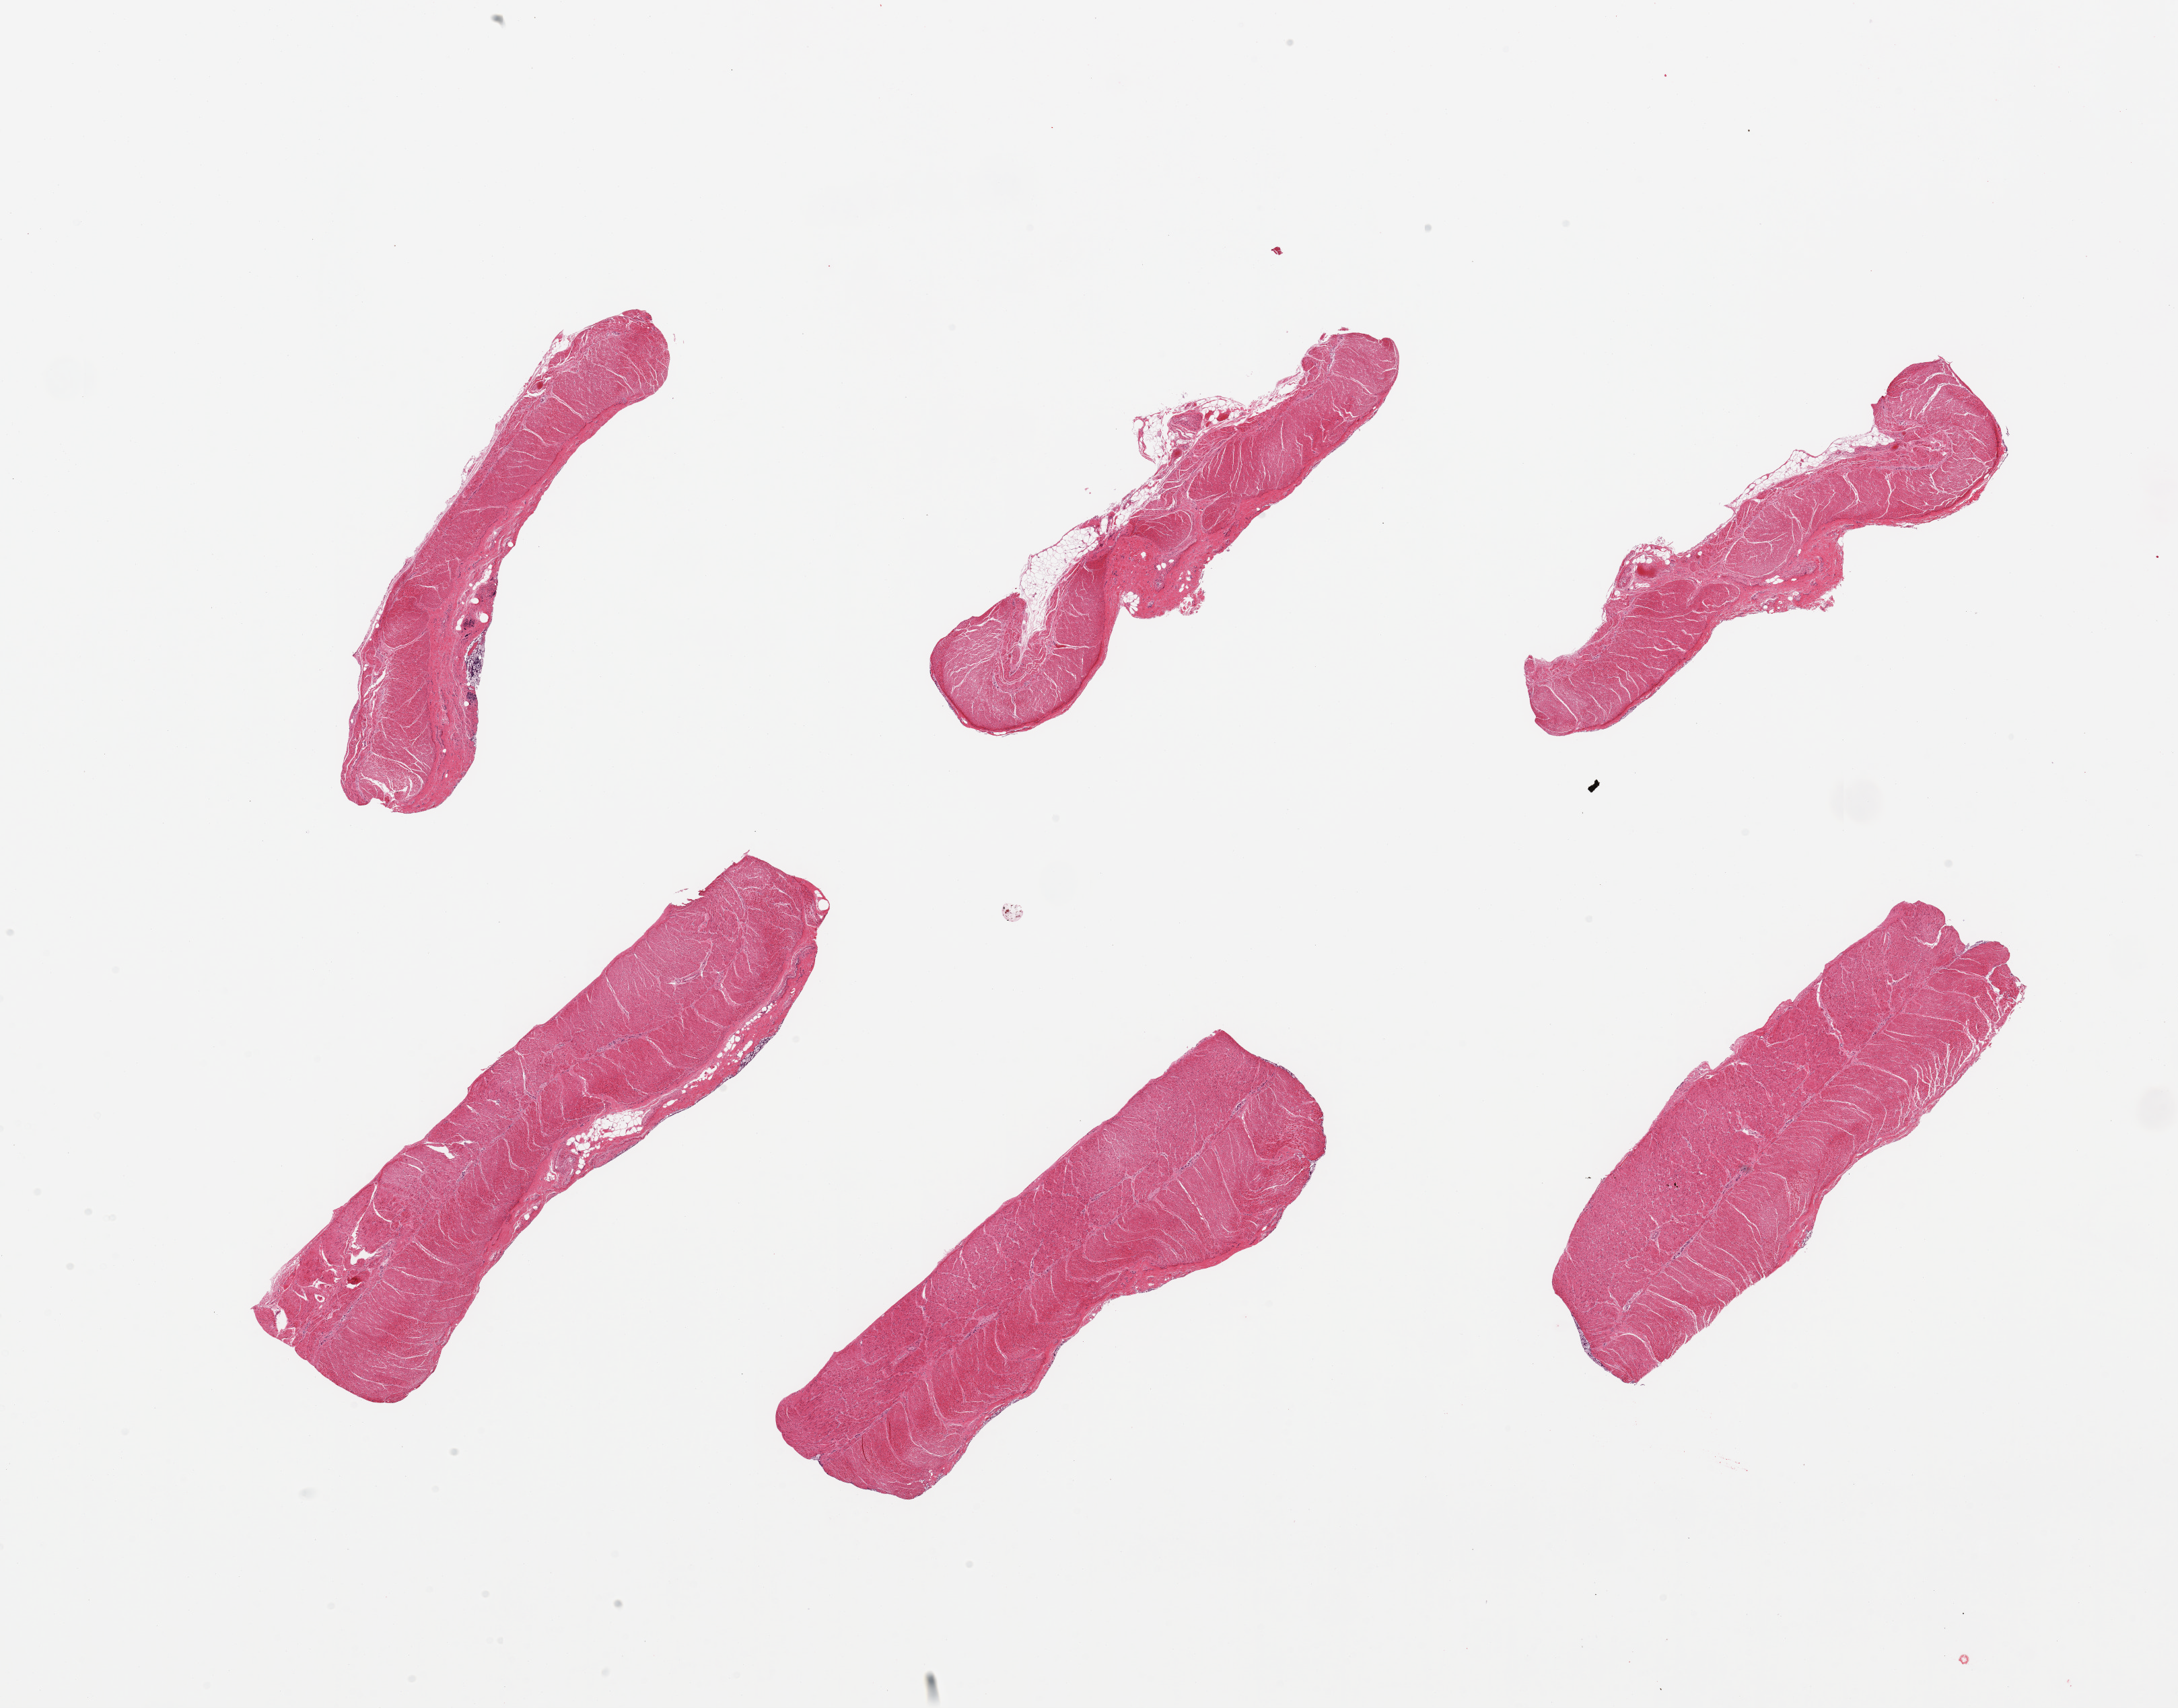
Haematoxylin and eosin whole-slide image, a low-resolution overview of the entire scanned area, about 25.6 x 20.1 mm (from a 20x scan). PAXgene-fixed paraffin-embedded (PFPE) section. Section of sigmoid colon (target tissue). Donor tissue sample. Female donor.
Review note (as recorded): 6 pieces.